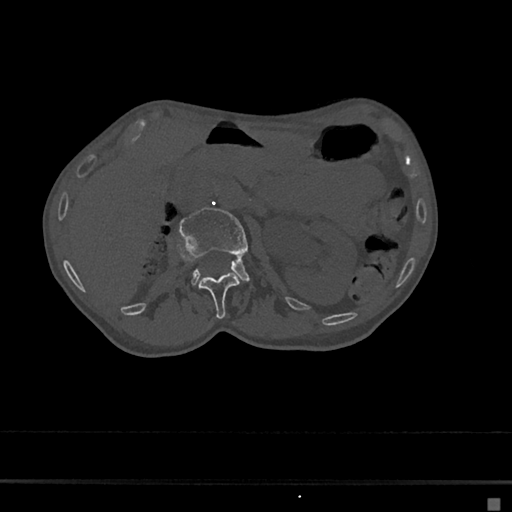
CT including the spine, one axial slice; bone window (W 1800 / L 400 HU); 512 × 512 image matrix, field of view 360 × 360 mm. Female patient, age 68 years. From the clinical record (not read from this slice): primary cancer: renal.
Structures marked on this image (semi-automatically segmented with operator editing):
- L1 vertebra: box from (x=199, y=273) to (x=239, y=319) px
- L2 vertebra: (x=180, y=207)–(x=249, y=284)